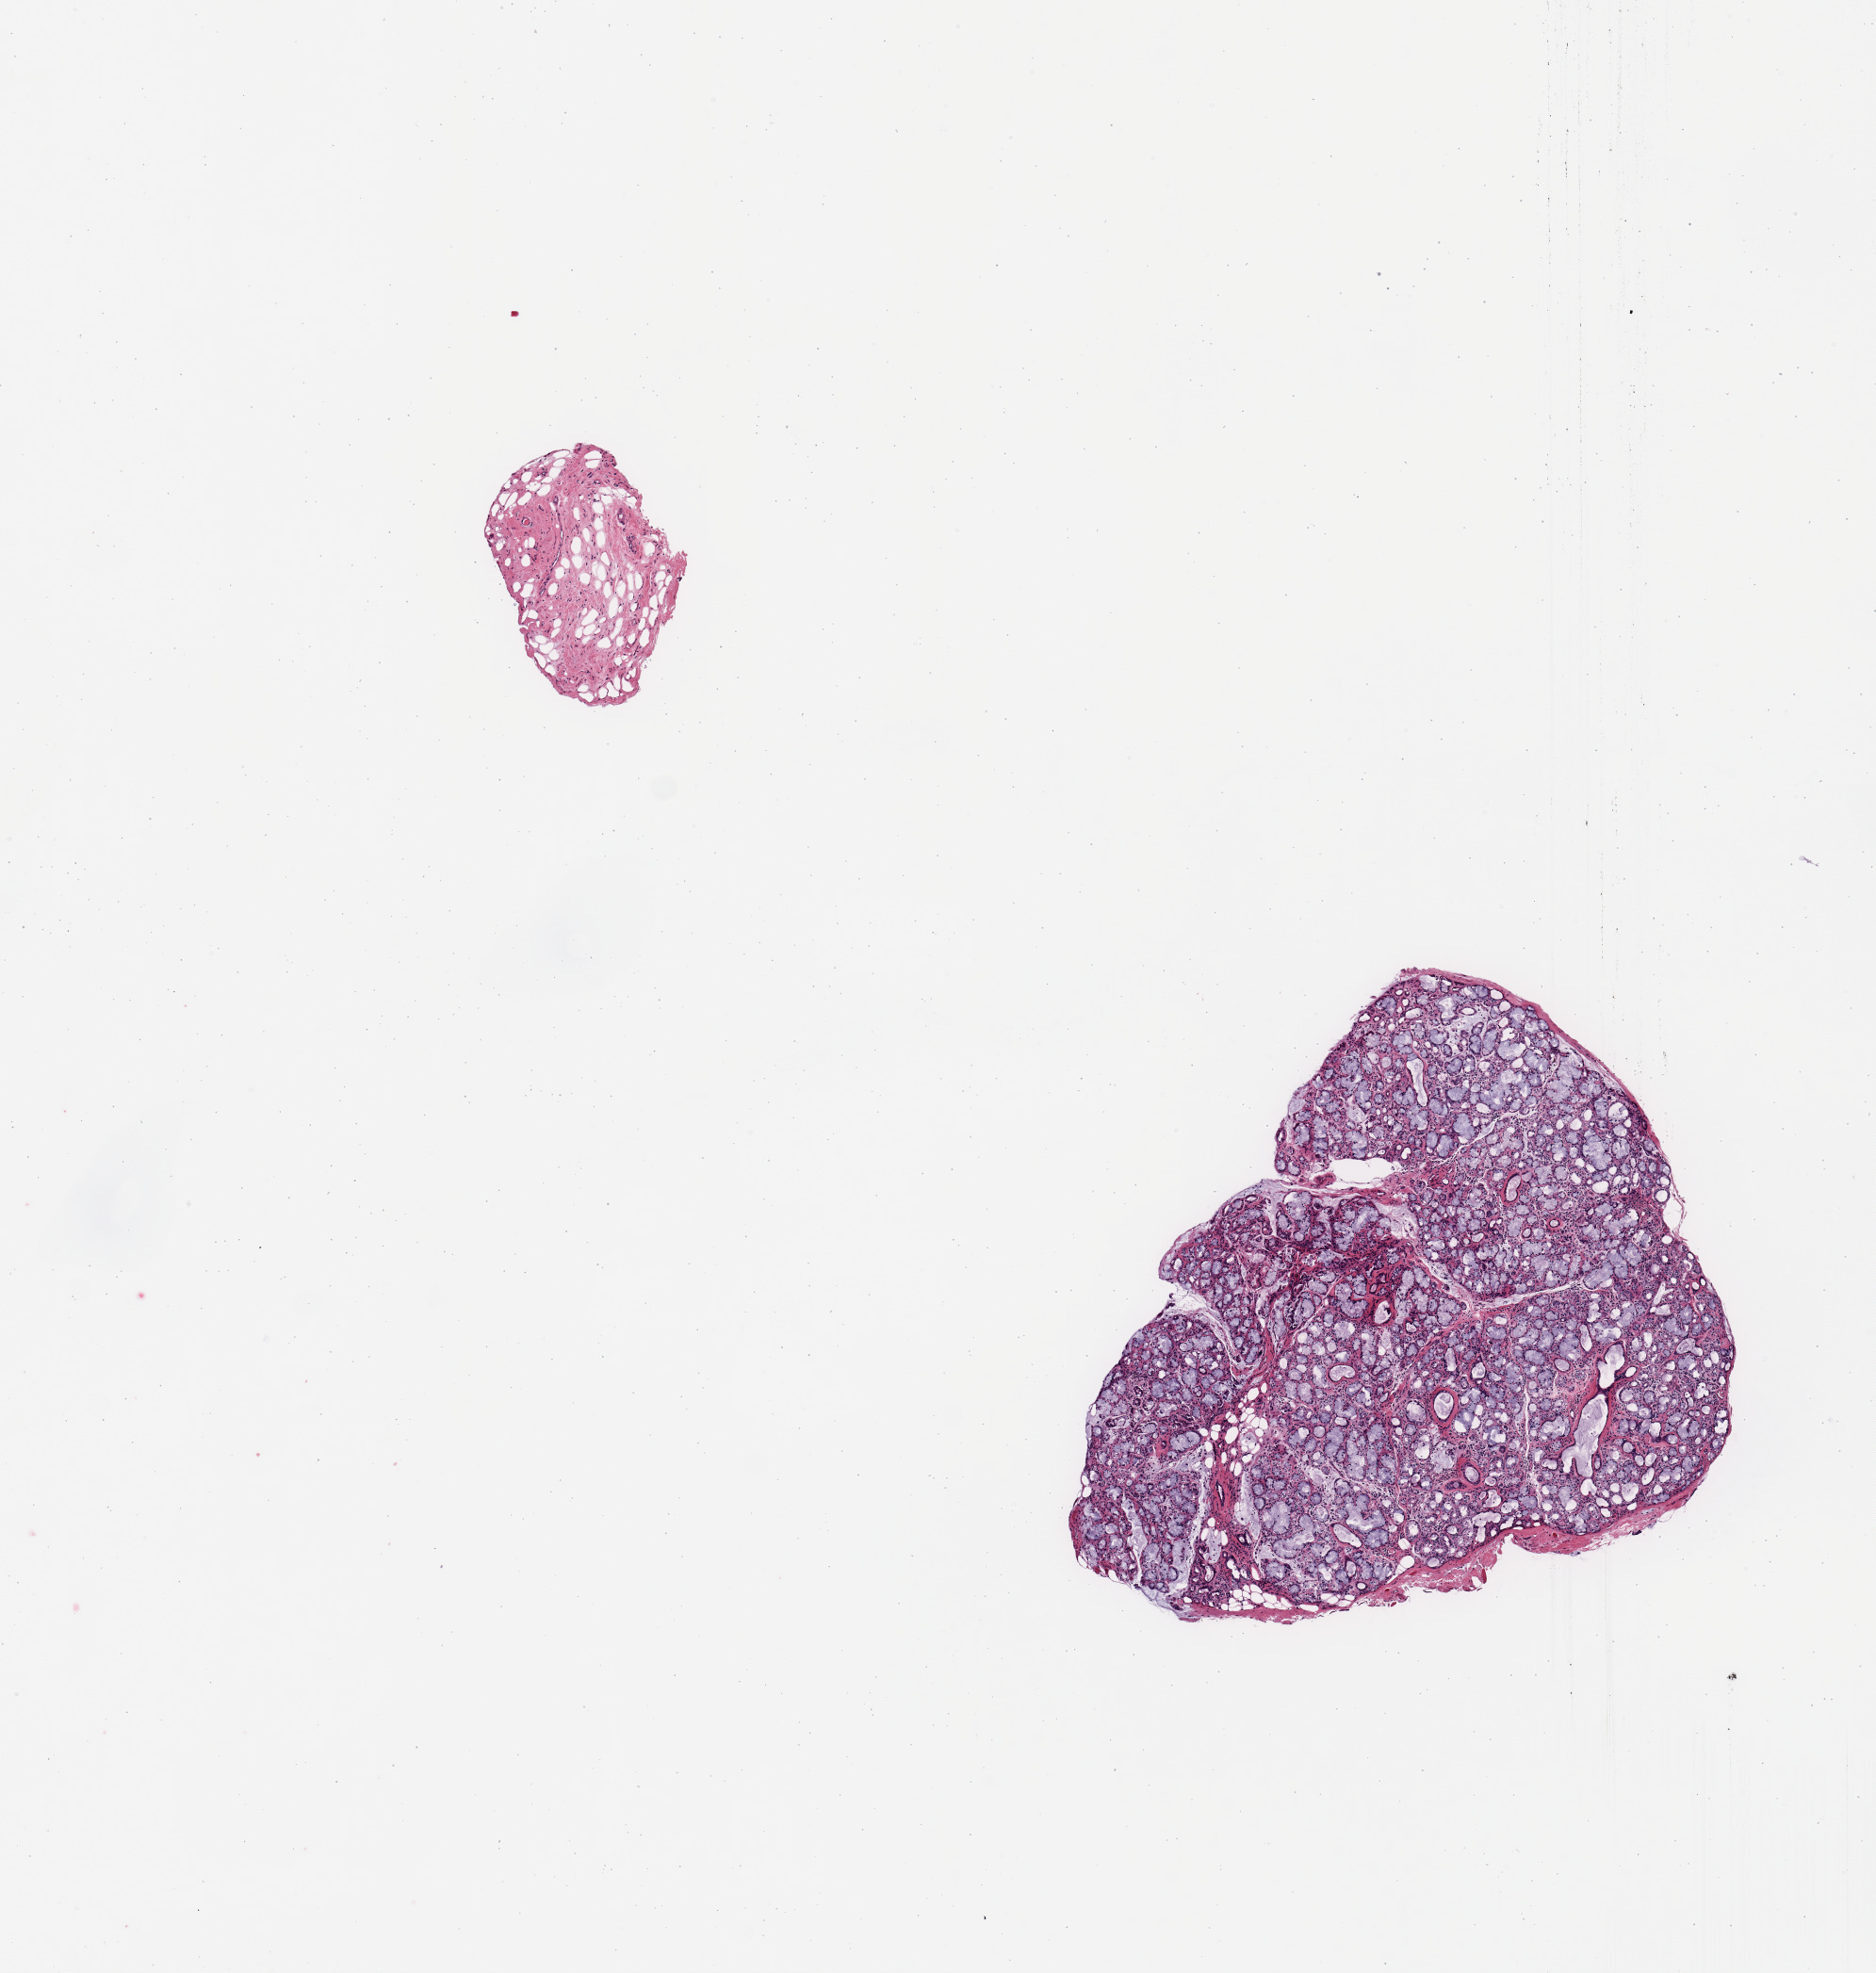
Haematoxylin and eosin whole-slide image, brightfield, low-resolution overview of the scanned area, about 7.9 x 8.3 mm (slide scanned at 20x). PAXgene-fixed, paraffin-embedded tissue. Target tissue: minor salivary gland. Donor tissue sample. Male donor.
- reviewer comment on this tissue sample: 2 pieces; 1 well dissected gland; smaller piece is fibrofatty tissue without glands